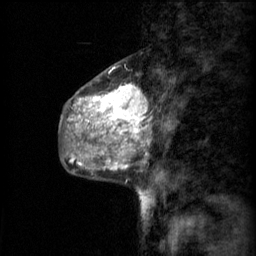
Breast MRI (dynamic contrast-enhanced), one sagittal slice; slice 24 of 60 in the series (ordered by position); 3 images stored at this slice position (order not interpretable as contrast timing); 1.5 T; TE 4.2 ms, TR 11 ms; 2 mm slice thickness; 256 × 256 image matrix, field of view 200 × 200 mm. Patient: female, 48 years.
Annotated regions visible in this slice (semi-automatically segmented with operator editing):
- analysis volume of interest (the breast-tissue region the enhancement analysis was run in; not a lesion): bounding box (x1, y1, x2, y2) in pixels: (69, 74, 149, 147)
- tumour enhancement mask (voxels above the 70 % enhancement threshold inside the analysis volume of interest): (75, 86, 143, 147)